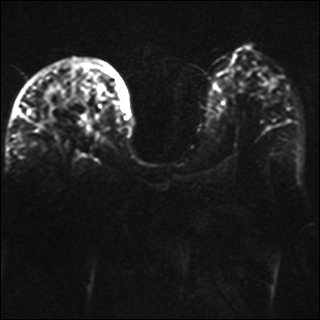
Breast MRI, one axial slice. Slice 19 of 42 in the series (ordered by position). Diffusion-weighted series; image 2 of 4 stored at this slice position (different b-values; order by instance number). 1.5 T. 4 mm slice thickness. 320 × 320 image matrix, field of view 330 × 330 mm. Female patient.
Annotated regions visible in this slice (outlined manually by an expert reader):
- tumour on diffusion-weighted imaging: bounding box [x1, y1, x2, y2] px = [48, 105, 56, 118]